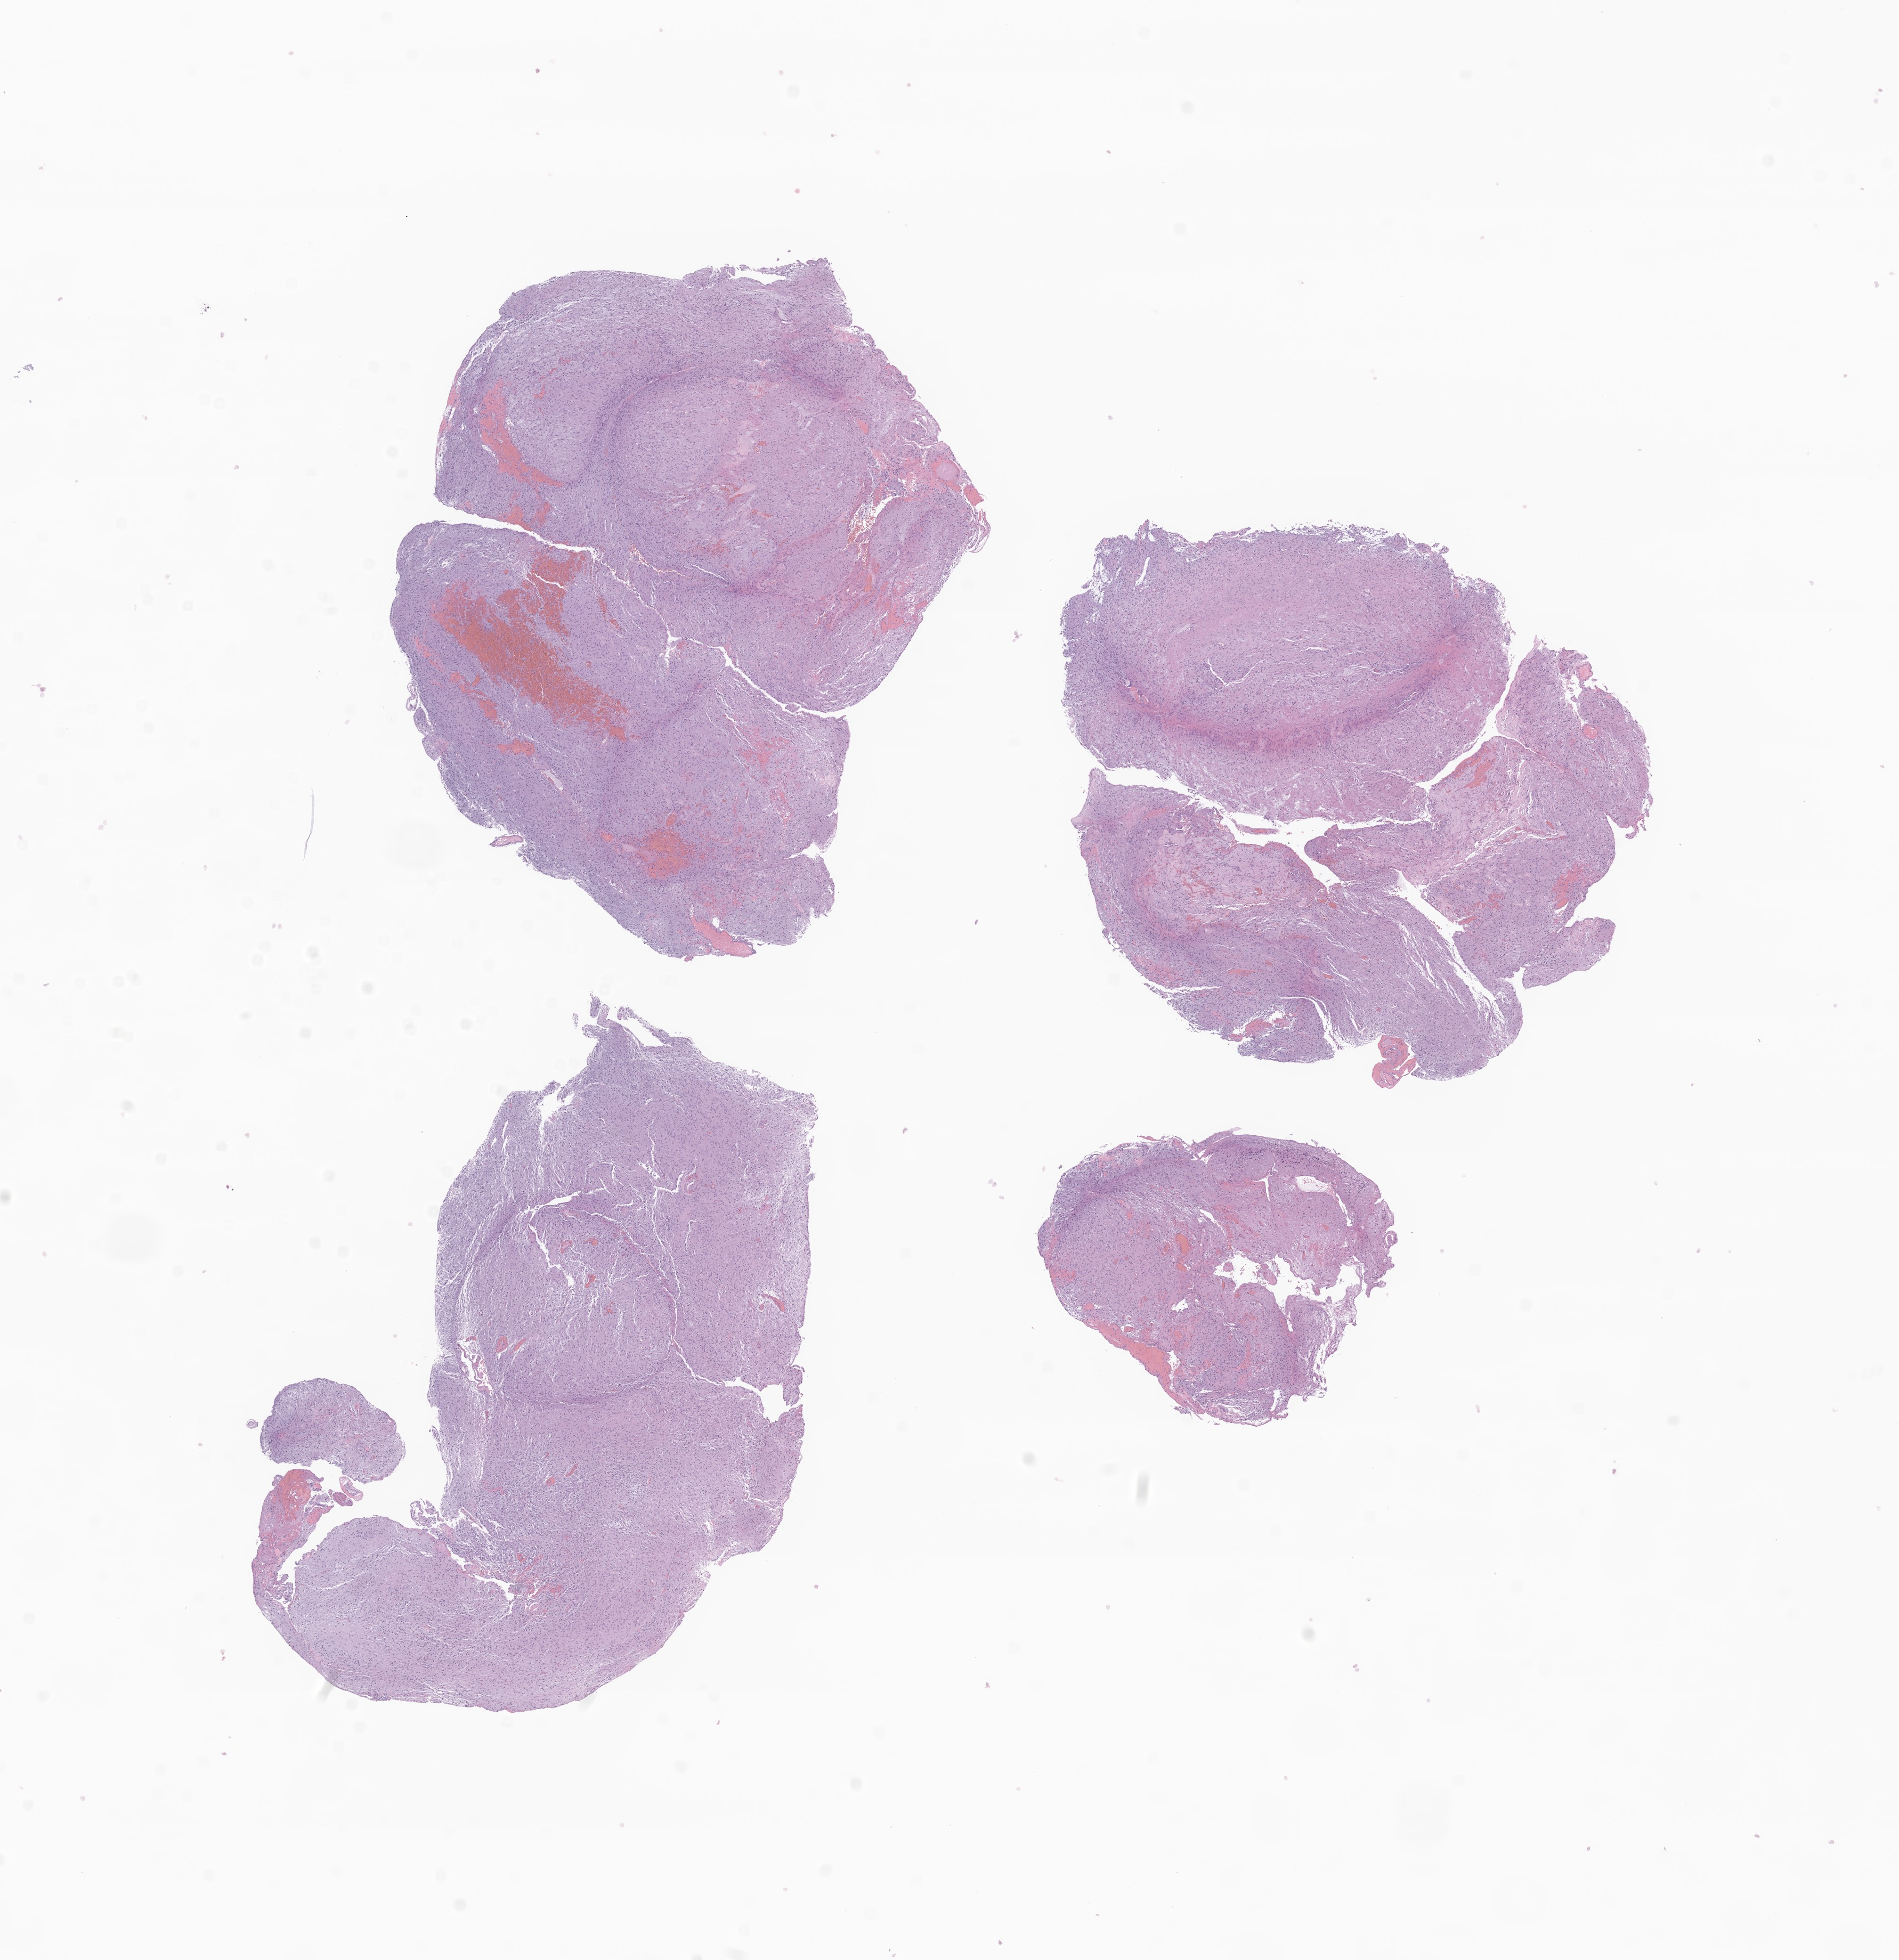
Whole-slide image, hematoxylin and eosin (H&E) stain of tumor tissue from the brain — a low-resolution overview of the entire scanned area, about 15.0 x 15.5 mm. FFPE section. Female patient, age 209 months.
Diagnosis: Astrocytoma, NOS.